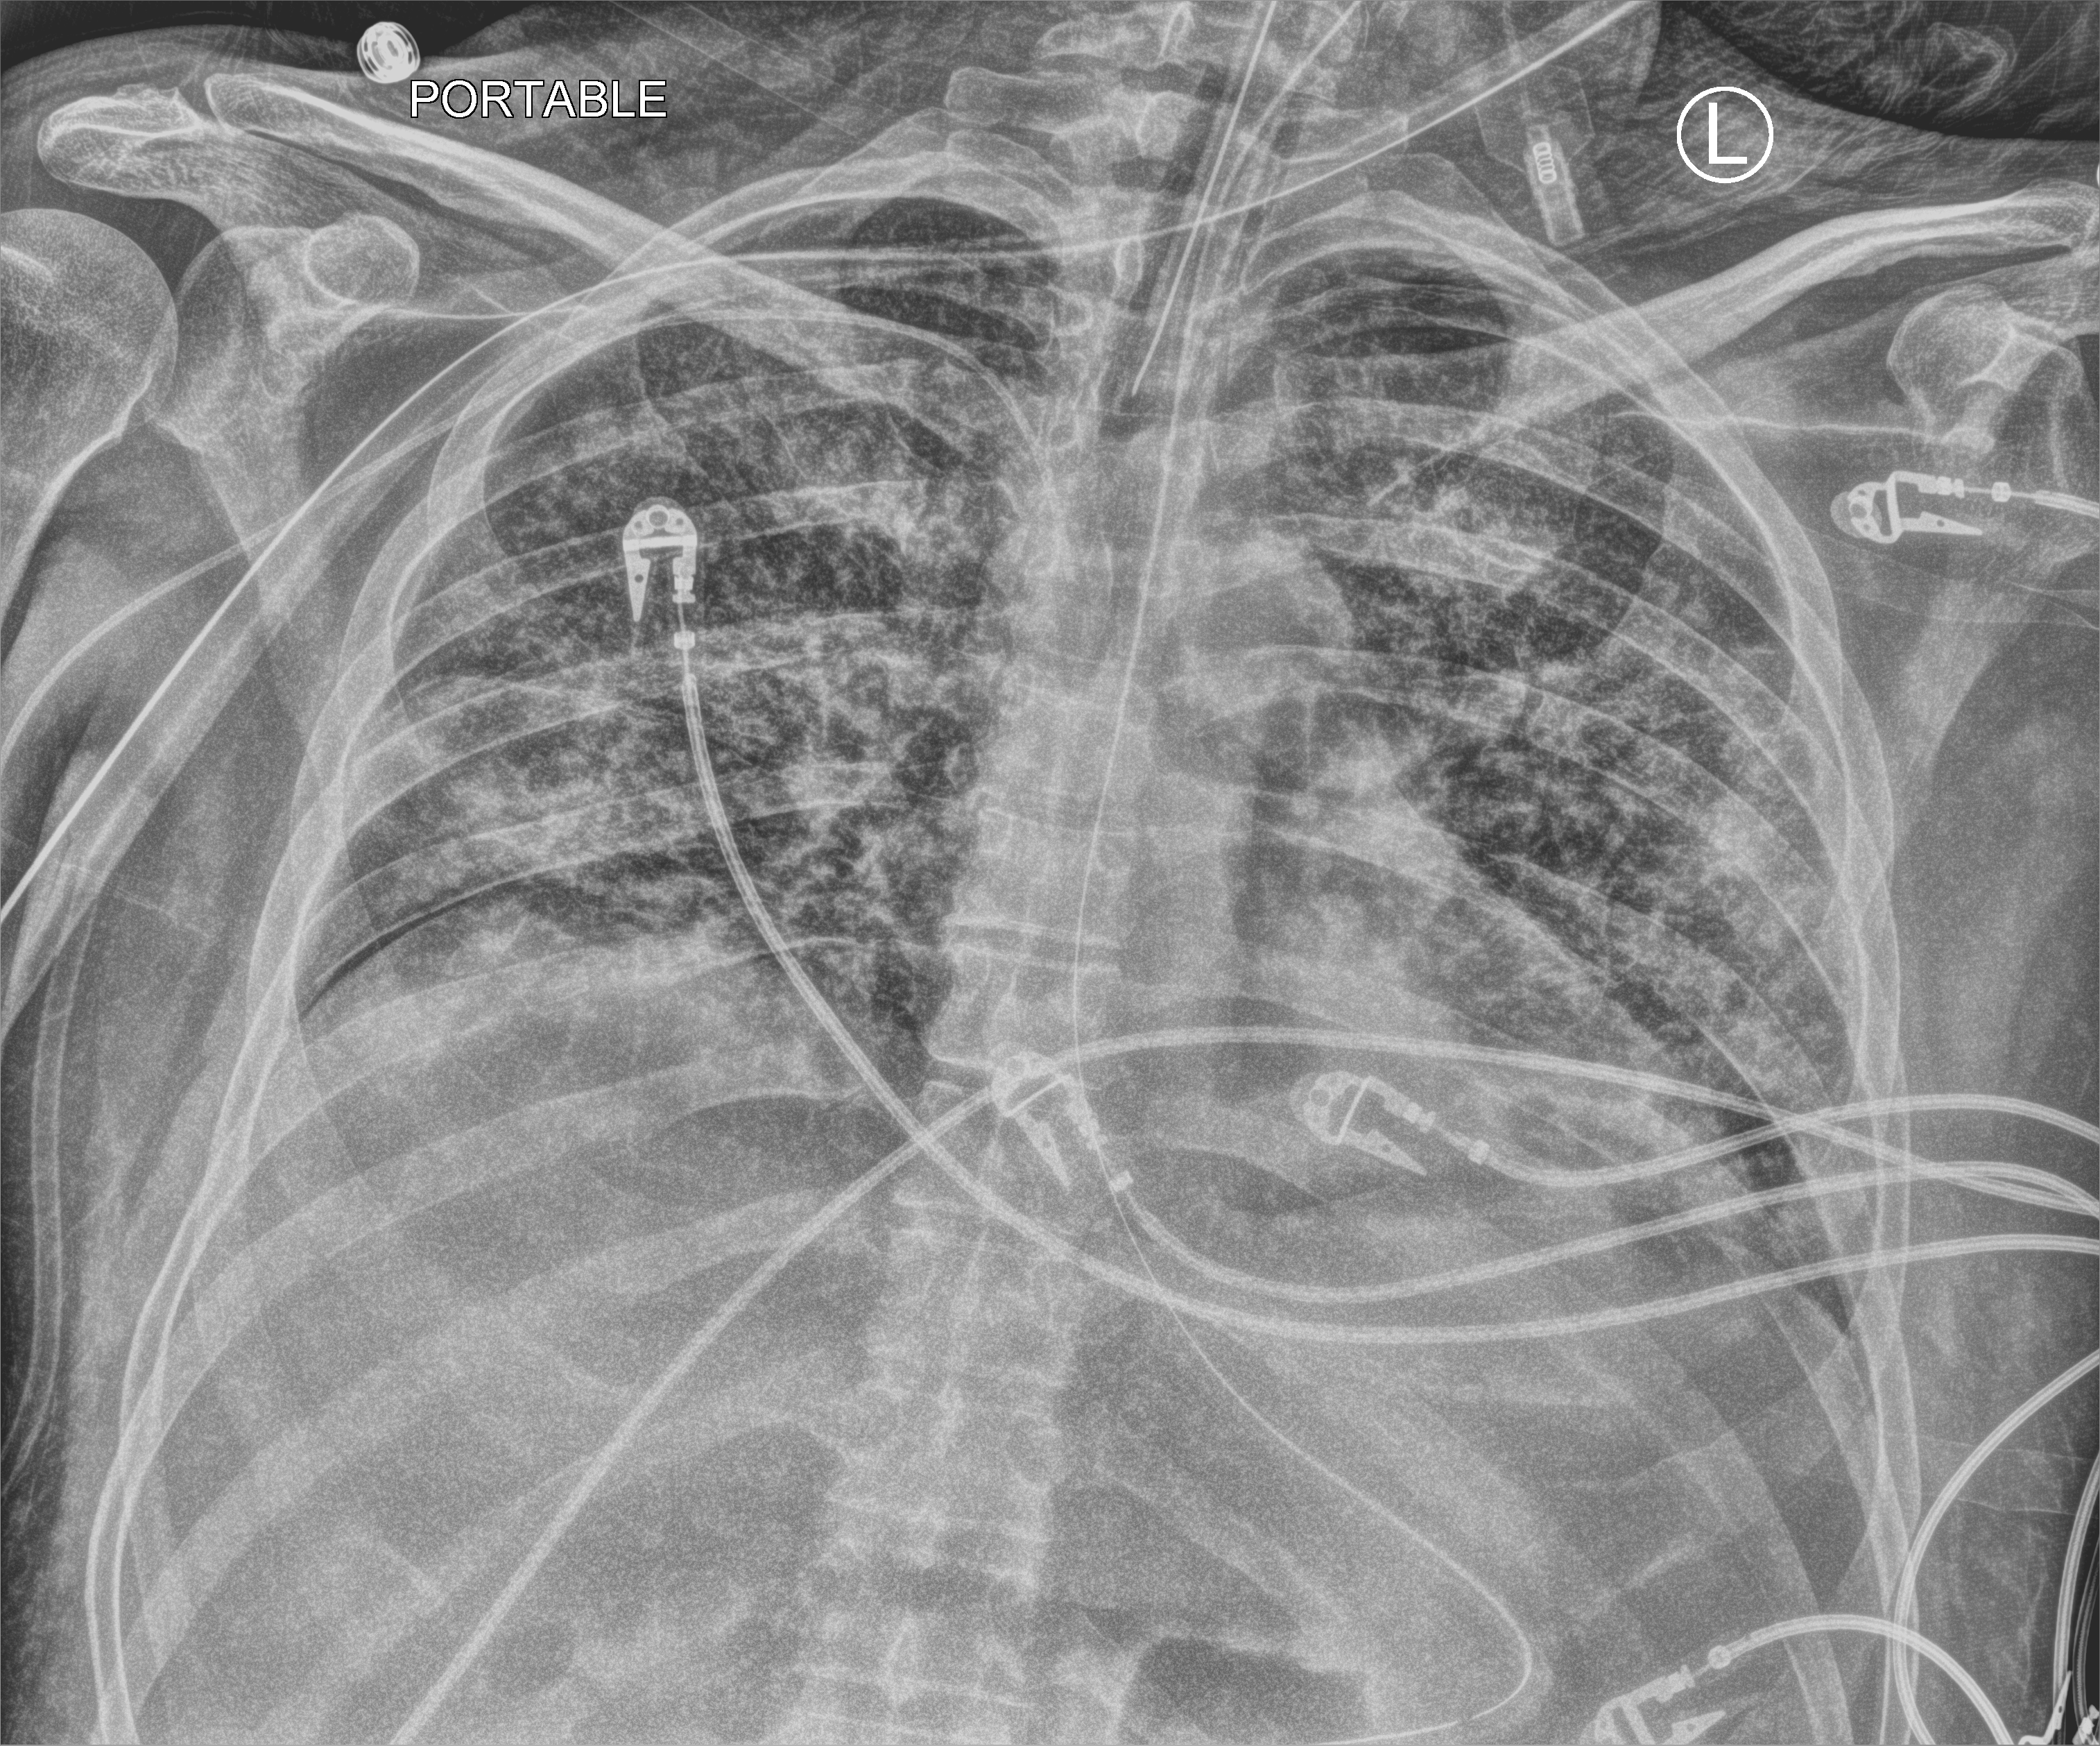
Portable chest radiograph. Male patient hospitalised with COVID-19, age 18–59 years.
Hospital-stay facts (about this admission, not read from this image; timing relative to this image not recorded): smoking status (admission record): never; admitted to intensive care during this hospital stay: yes; mechanically ventilated during this hospital stay: yes.